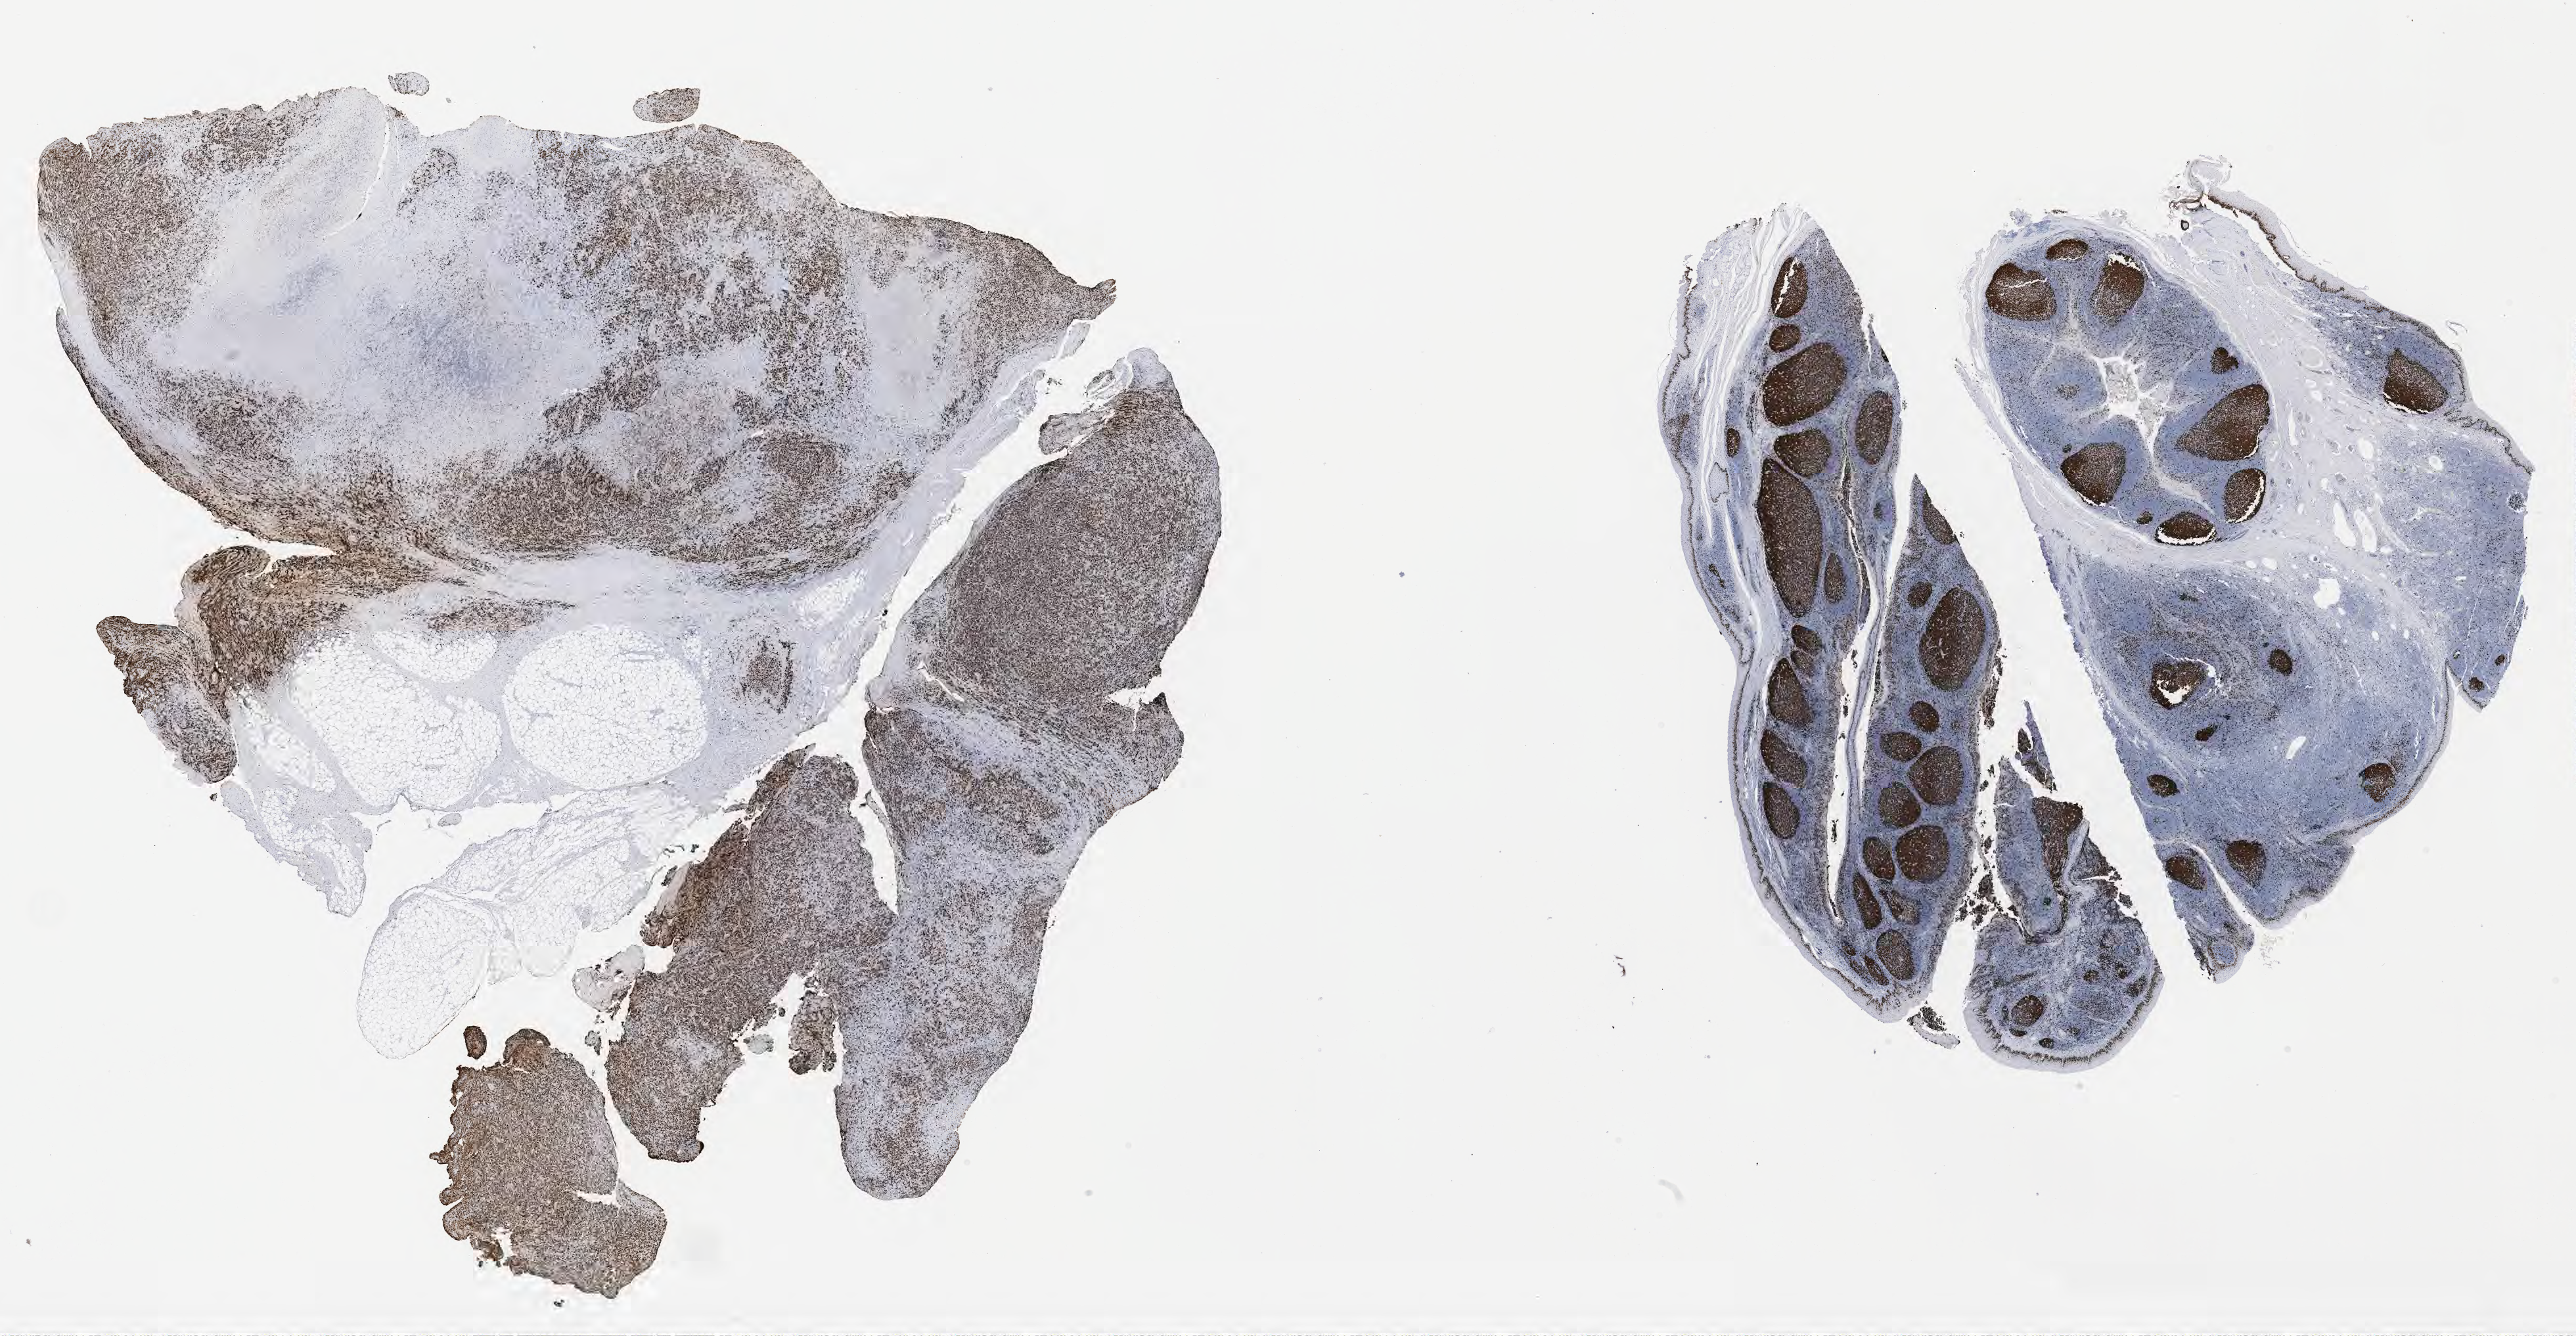
Whole-slide image, immunohistochemical stain for Ki-67 — whole scanned area (about 31.7 x 16.4 mm) shown as a low-resolution overview. Specimen: tumor tissue. Patient: female, aged 46.
- histologic diagnosis: Diffuse large B-cell lymphoma, NOS